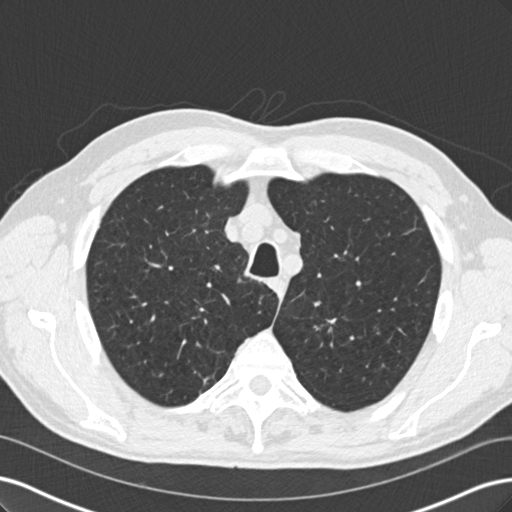
Low-dose screening chest CT, one axial slice. Lung window (W 1500 / L -600 HU). 2 mm slice thickness. 512 × 512 image matrix, field of view 360 × 360 mm.
Outlined on this slice (expert manual segmentation):
- lesion 1 (tumor, upper lobe of left lung): box from (x=315, y=318) to (x=337, y=333) px